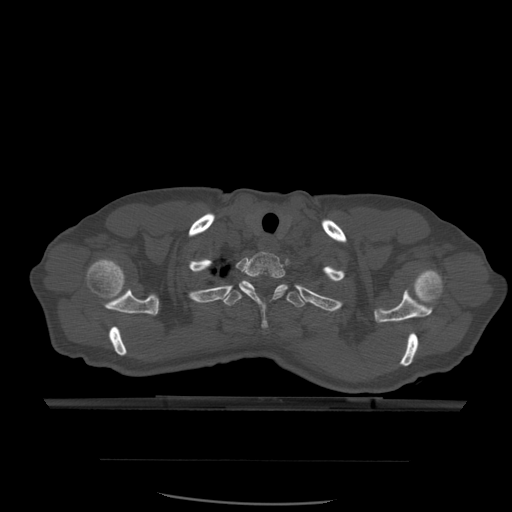
CT including the spine, one axial slice. Slice 465 of 574 in the series (ordered by position). Bone window (W 1800 / L 400 HU). 512 × 512 image matrix, field of view 392 × 392 mm. Patient age 48 years. Case-level facts recorded for this patient, not image findings: primary cancer: lung; vertebrae with lytic lesions (as recorded): T11.
Outlined on this slice (semi-automatic segmentation, software-assisted and operator-edited):
- T1 vertebra: bounding box [x1, y1, x2, y2] px = [239, 252, 286, 328]
- T2 vertebra: [222, 280, 307, 308]